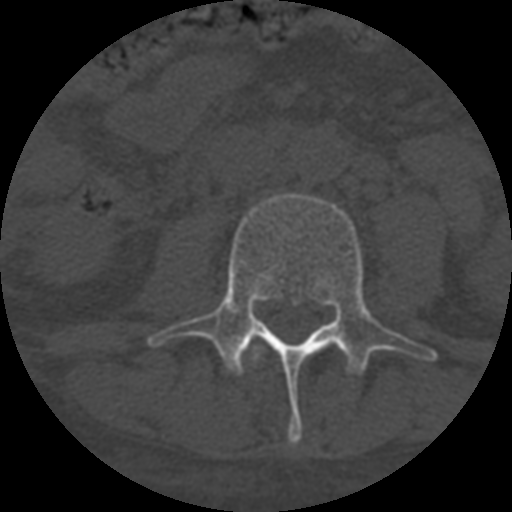
CT including the spine, one axial slice. Position 237 of 708 along the scan axis. Reconstruction kernel STANDARD. 120 kVp. One of 3 acquisitions stored at this slice position. Bone window (W 1800 / L 400 HU). 512 × 512 image matrix, field of view 160 × 160 mm. Patient age 55 years. Case-level facts recorded for this patient, not image findings: primary cancer: colon; vertebrae with lytic lesions (as recorded): T12, L1, L5.
Structures marked on this image (semi-automatically segmented with operator editing):
- L2 vertebra: box from (x=250, y=345) to (x=265, y=365) px
- L3 vertebra: (x=147, y=193)–(x=437, y=443)